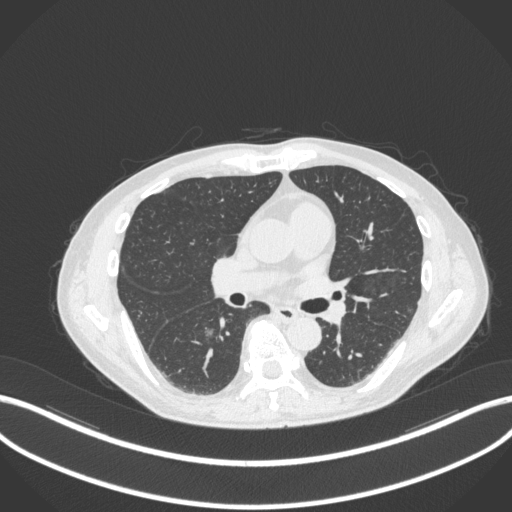
Chest CT, one axial slice; slice 175 of 324 in the series (ordered by position); reconstruction kernel B31f; 120 kVp; lung window (W 1500 / L -600 HU); 1 mm slice thickness; 512 × 512 image matrix, field of view 400 × 400 mm. Male patient, age 61 years. Case-level facts recorded for this patient, not image findings: clinical TNM (as recorded): T1c N0 M0.
Outlined on this slice (bounding box drawn by a radiologist):
- lung tumour (recorded histology: adenocarcinoma): bounding box <204,323,215,339> (left, top, right, bottom; pixels)